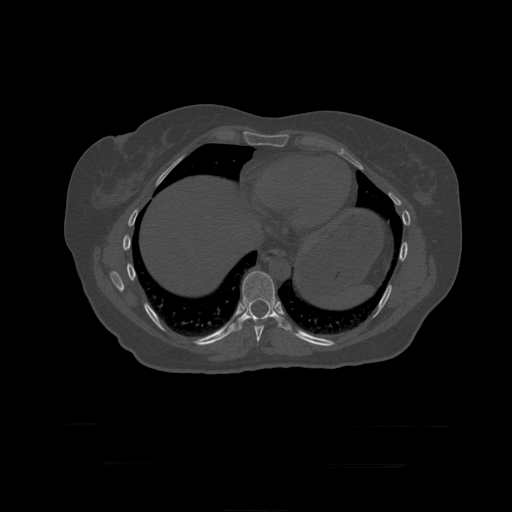
CT including the spine, one axial slice. Slice 249 of 399 in the series (ordered by position). Reconstruction kernel STANDARD. Bone window (W 1800 / L 400 HU). 1.25 mm slice thickness. 512 × 512 image matrix, field of view 450 × 450 mm. Patient age 41 years. From the clinical record (not read from this slice): primary cancer: breast.
Annotated regions visible in this slice (semi-automatically segmented with operator editing):
- T10 vertebra: box from (x=232, y=271) to (x=290, y=332) px
- T9 vertebra: (x=254, y=325)–(x=265, y=342)